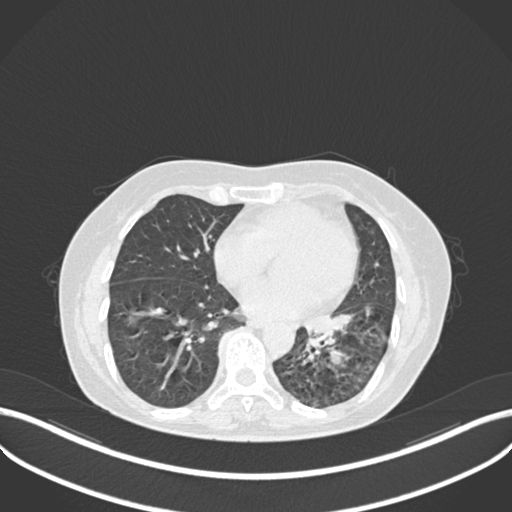
Chest CT, one axial slice. Position 104 of 270 along the scan axis. 120 kVp. Lung window (W 1500 / L -600 HU). 1 mm slice thickness. 512 × 512 image matrix, field of view 400 × 400 mm. Female patient, age 63 years. From the clinical record (not read from this slice): clinical TNM (as recorded): T1b N0 M0.
Outlined on this slice (rectangle marked by the reading radiologist):
- lung tumour (recorded histology: adenocarcinoma): bounding box <302,310,352,343> (left, top, right, bottom; pixels)